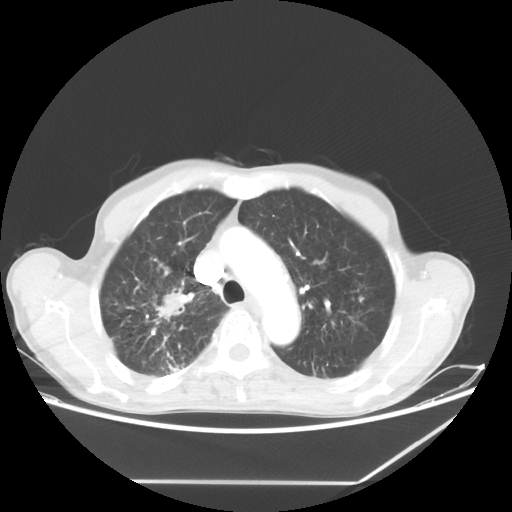
Chest CT, one axial slice. Slice 47 of 65 in the series (ordered by position). 80 kVp. Lung window (W 1500 / L -600 HU). 5 mm slice thickness. 512 × 512 image matrix, field of view 397 × 397 mm. Male patient, age 68 years. From the clinical record (not read from this slice): clinical TNM (as recorded): T3 N3 M0.
Outlined on this slice (bounding box drawn by a radiologist):
- lung tumour (recorded histology: adenocarcinoma): bounding box <148,286,191,326> (left, top, right, bottom; pixels)